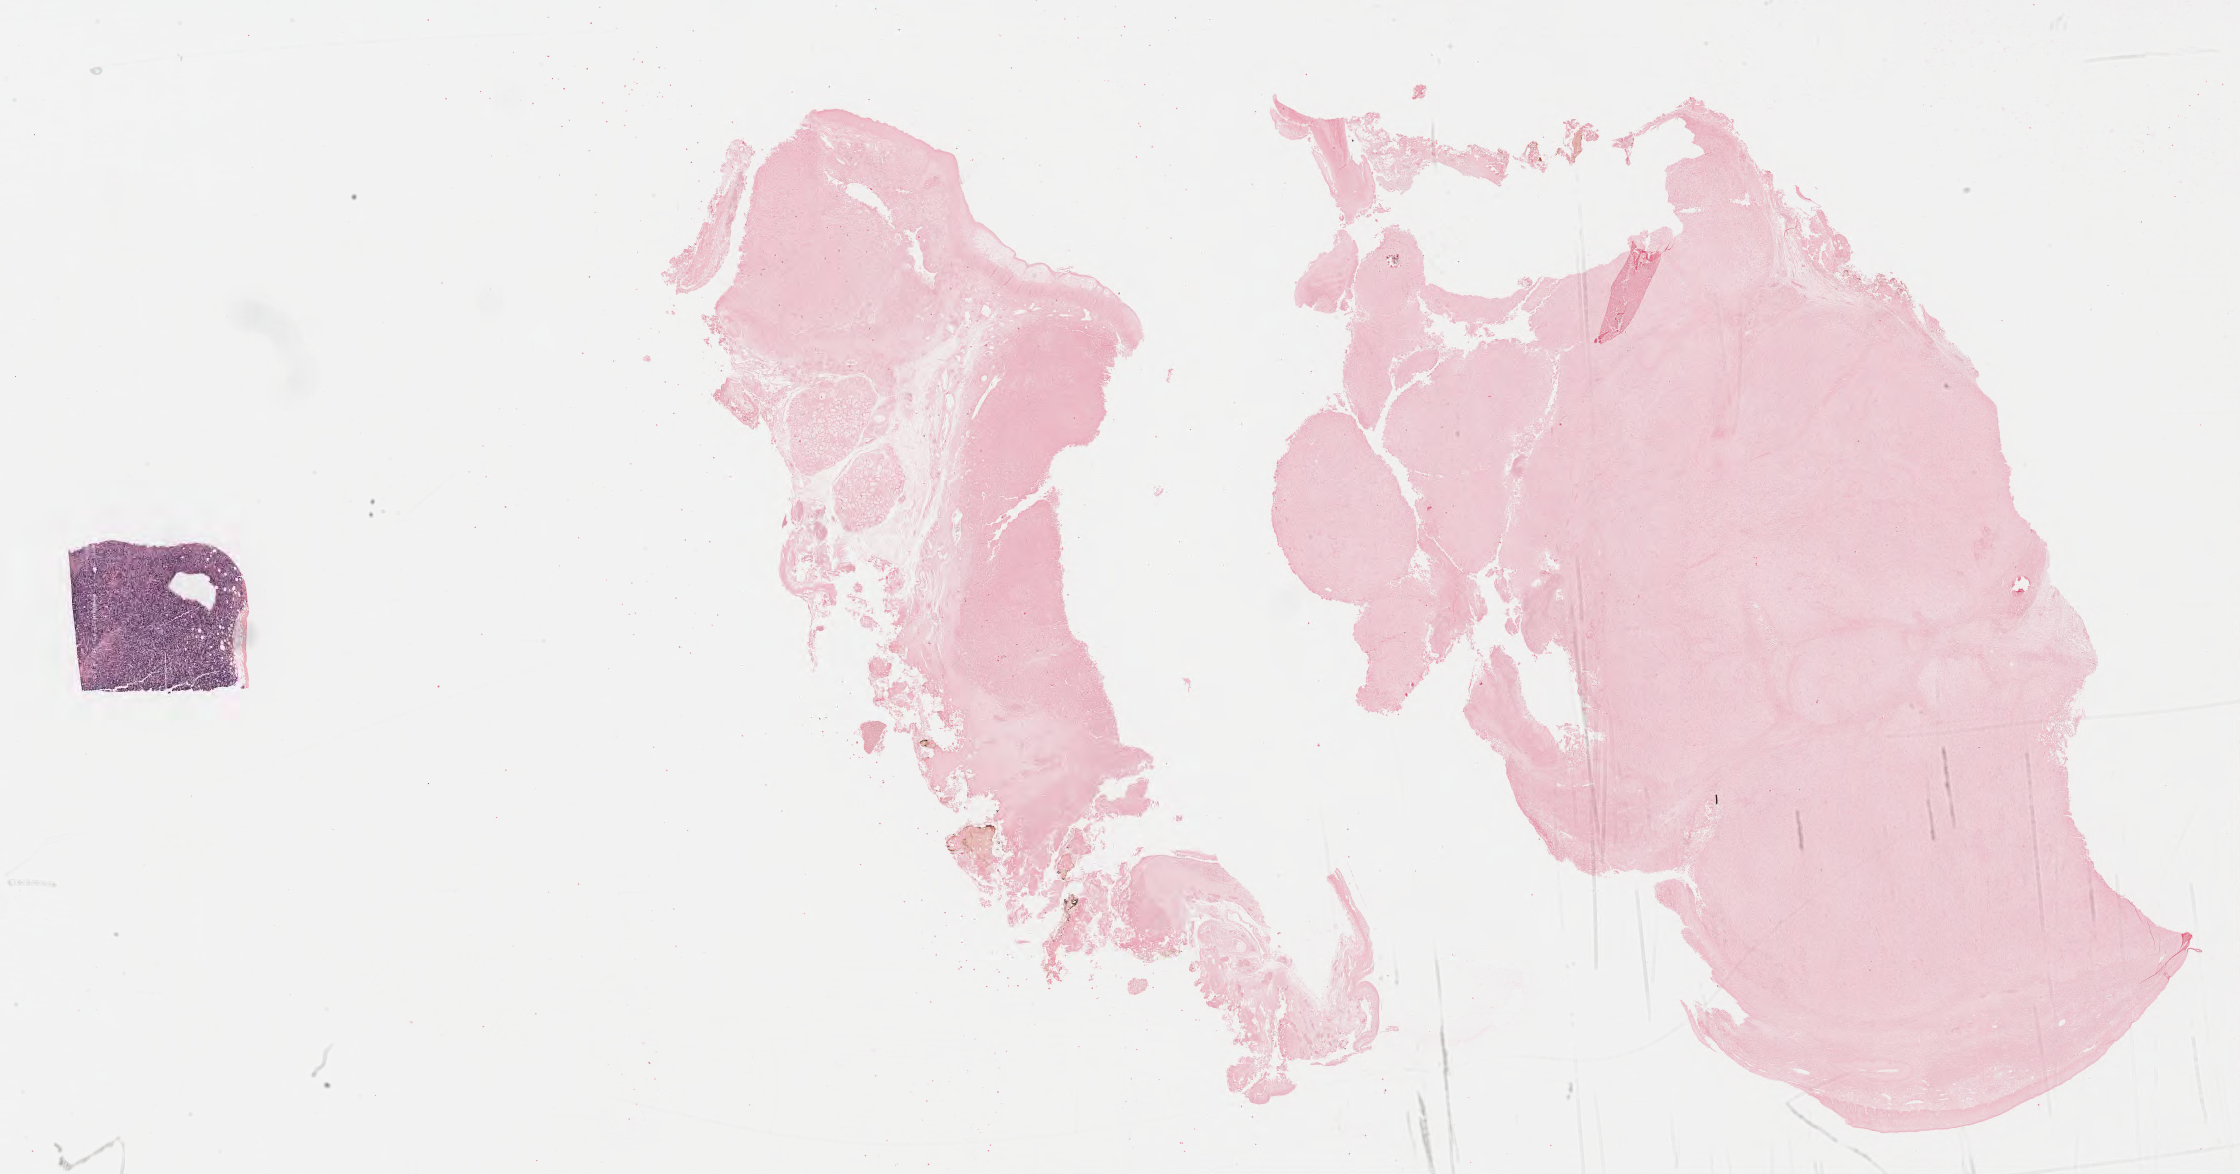
In-situ hybridisation whole-slide image, Epstein–Barr virus-encoded RNA (EBER) probe — whole scanned area (about 36.2 x 19.0 mm) shown as a low-resolution overview. Specimen: tumor tissue. Site: lymph node. Patient male; aged 56.
Histologic diagnosis: Diffuse large B-cell lymphoma, NOS.